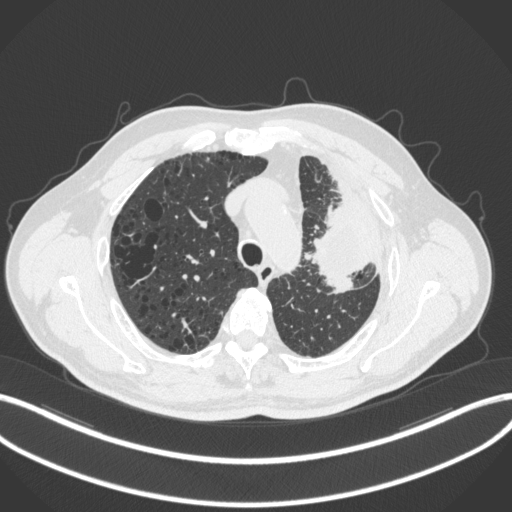
Chest CT, one axial slice; slice 231 of 286 in the series (ordered by position); reconstruction kernel B31f; lung window (W 1500 / L -600 HU); 1 mm slice thickness; 512 × 512 image matrix, field of view 400 × 400 mm. Male patient, age 68 years. From the clinical record (not read from this slice): clinical TNM (as recorded): T3 N3 M1.
Annotated regions visible in this slice (bounding box drawn by a radiologist):
- lung tumour (recorded histology: adenocarcinoma): bounding box <309,181,376,293> (left, top, right, bottom; pixels)